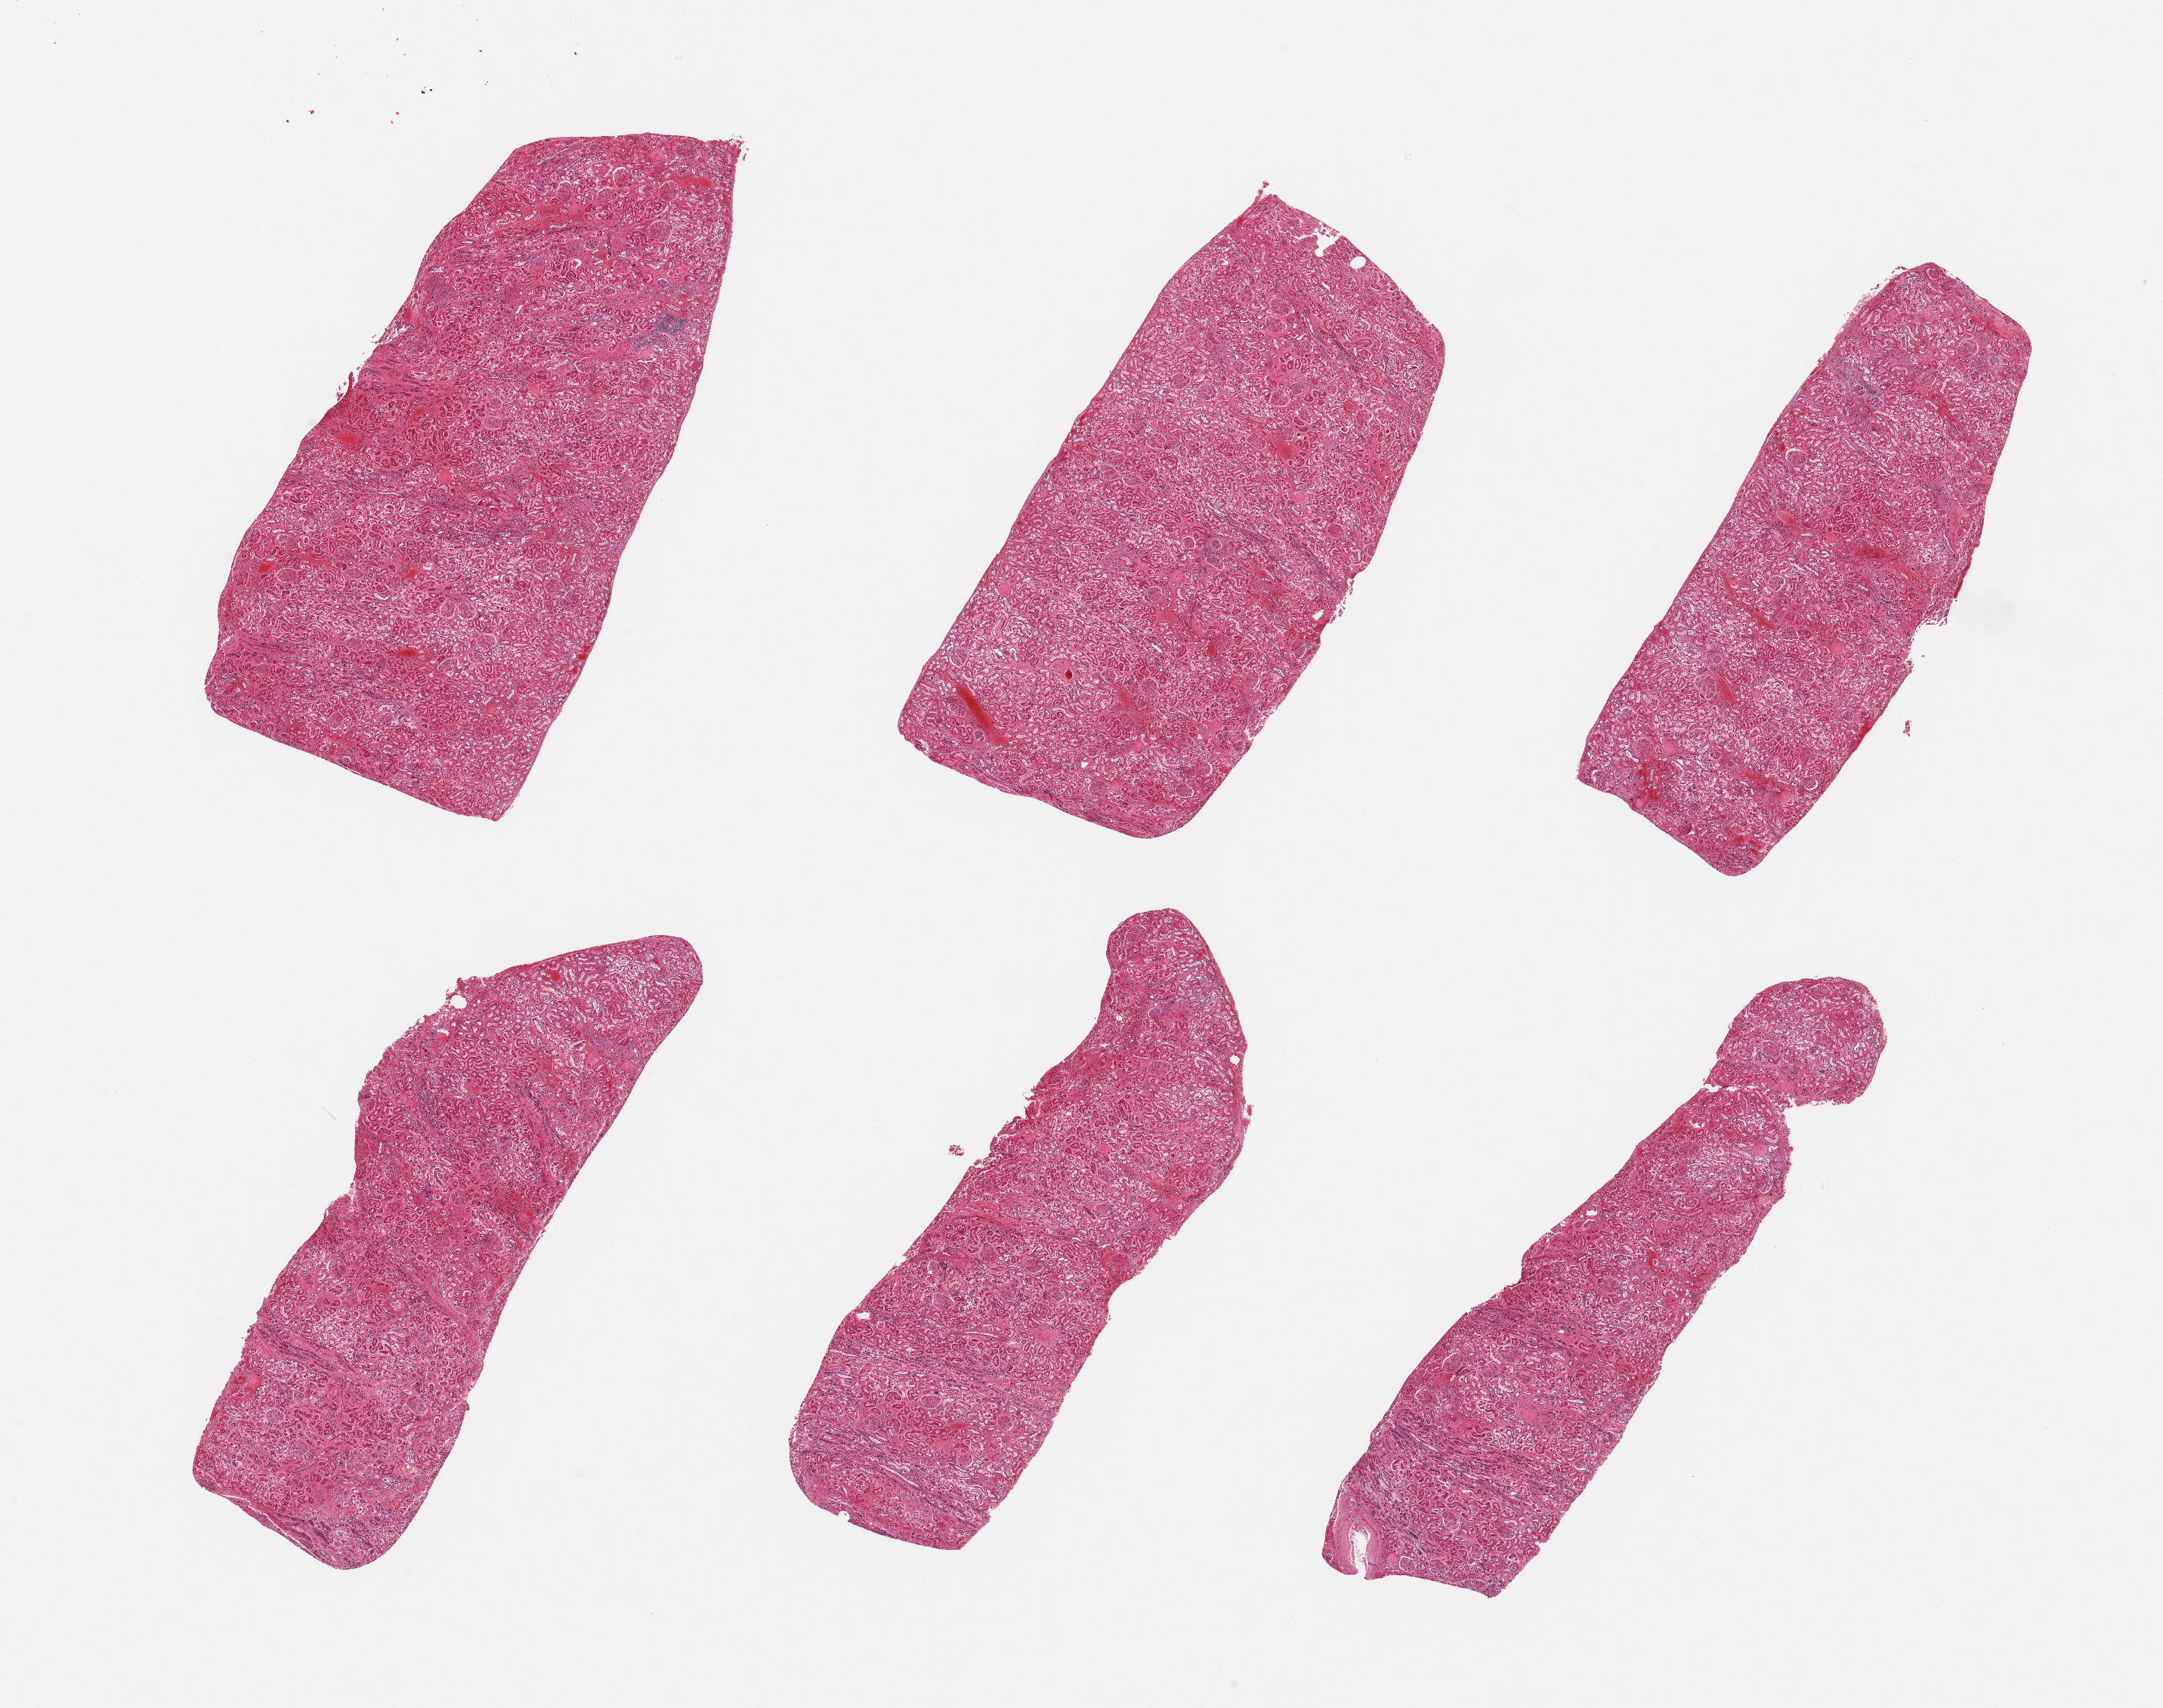
Whole-slide image, haematoxylin and eosin stain — a low-resolution overview of the entire scanned area, about 22.6 x 17.9 mm (from a 20x scan). PAXgene-fixed paraffin-embedded (PFPE) section. Sampled site (target tissue): renal cortex. Tissue donor sample. Female donor.
• reviewer comment on this tissue sample: 6 pieces, glomeruli present; advanced tubular autolysis